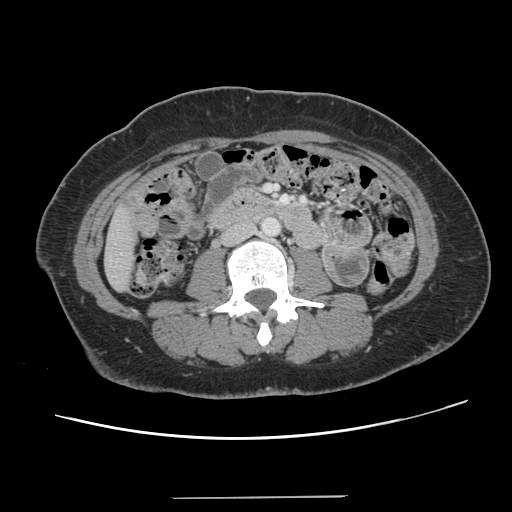
Contrast-enhanced abdominal CT, one axial slice; position 25 of 141 along the scan axis; 120 kVp; intravenous contrast given; soft-tissue window (W 400 / L 40 HU); 2.5 mm slice thickness; 512 × 512 image matrix. Female patient, age 53 years. Case-level facts recorded for this patient, not image findings: diagnosis: colorectal cancer liver metastases, imaged before liver resection; multiple liver metastases: no.
Annotated regions visible in this slice (manually delineated by an expert):
- liver: bounding box <105,208,136,290> (left, top, right, bottom; pixels)
- planned liver remnant (the part of the liver to remain after resection): <106,208,136,290>